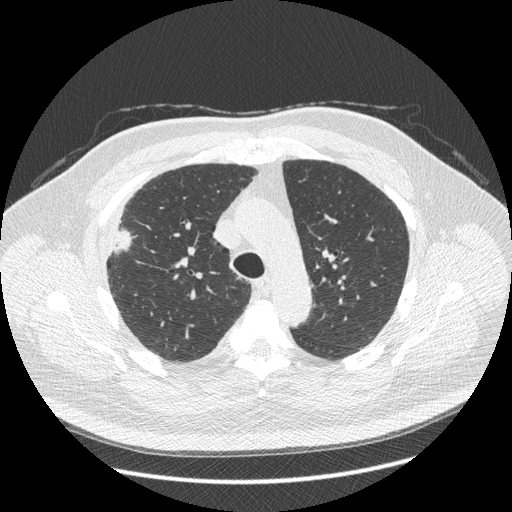
Low-dose screening chest CT, one axial slice. Slice 311 of 426 in the series (ordered by position). 120 kVp. Lung window (W 1500 / L -600 HU). 512 × 512 image matrix.
Structures marked on this image (expert manual segmentation):
- lesion 1 (tumor, upper lobe of right lung): bounding box (x1, y1, x2, y2) in pixels: (114, 230, 132, 252)